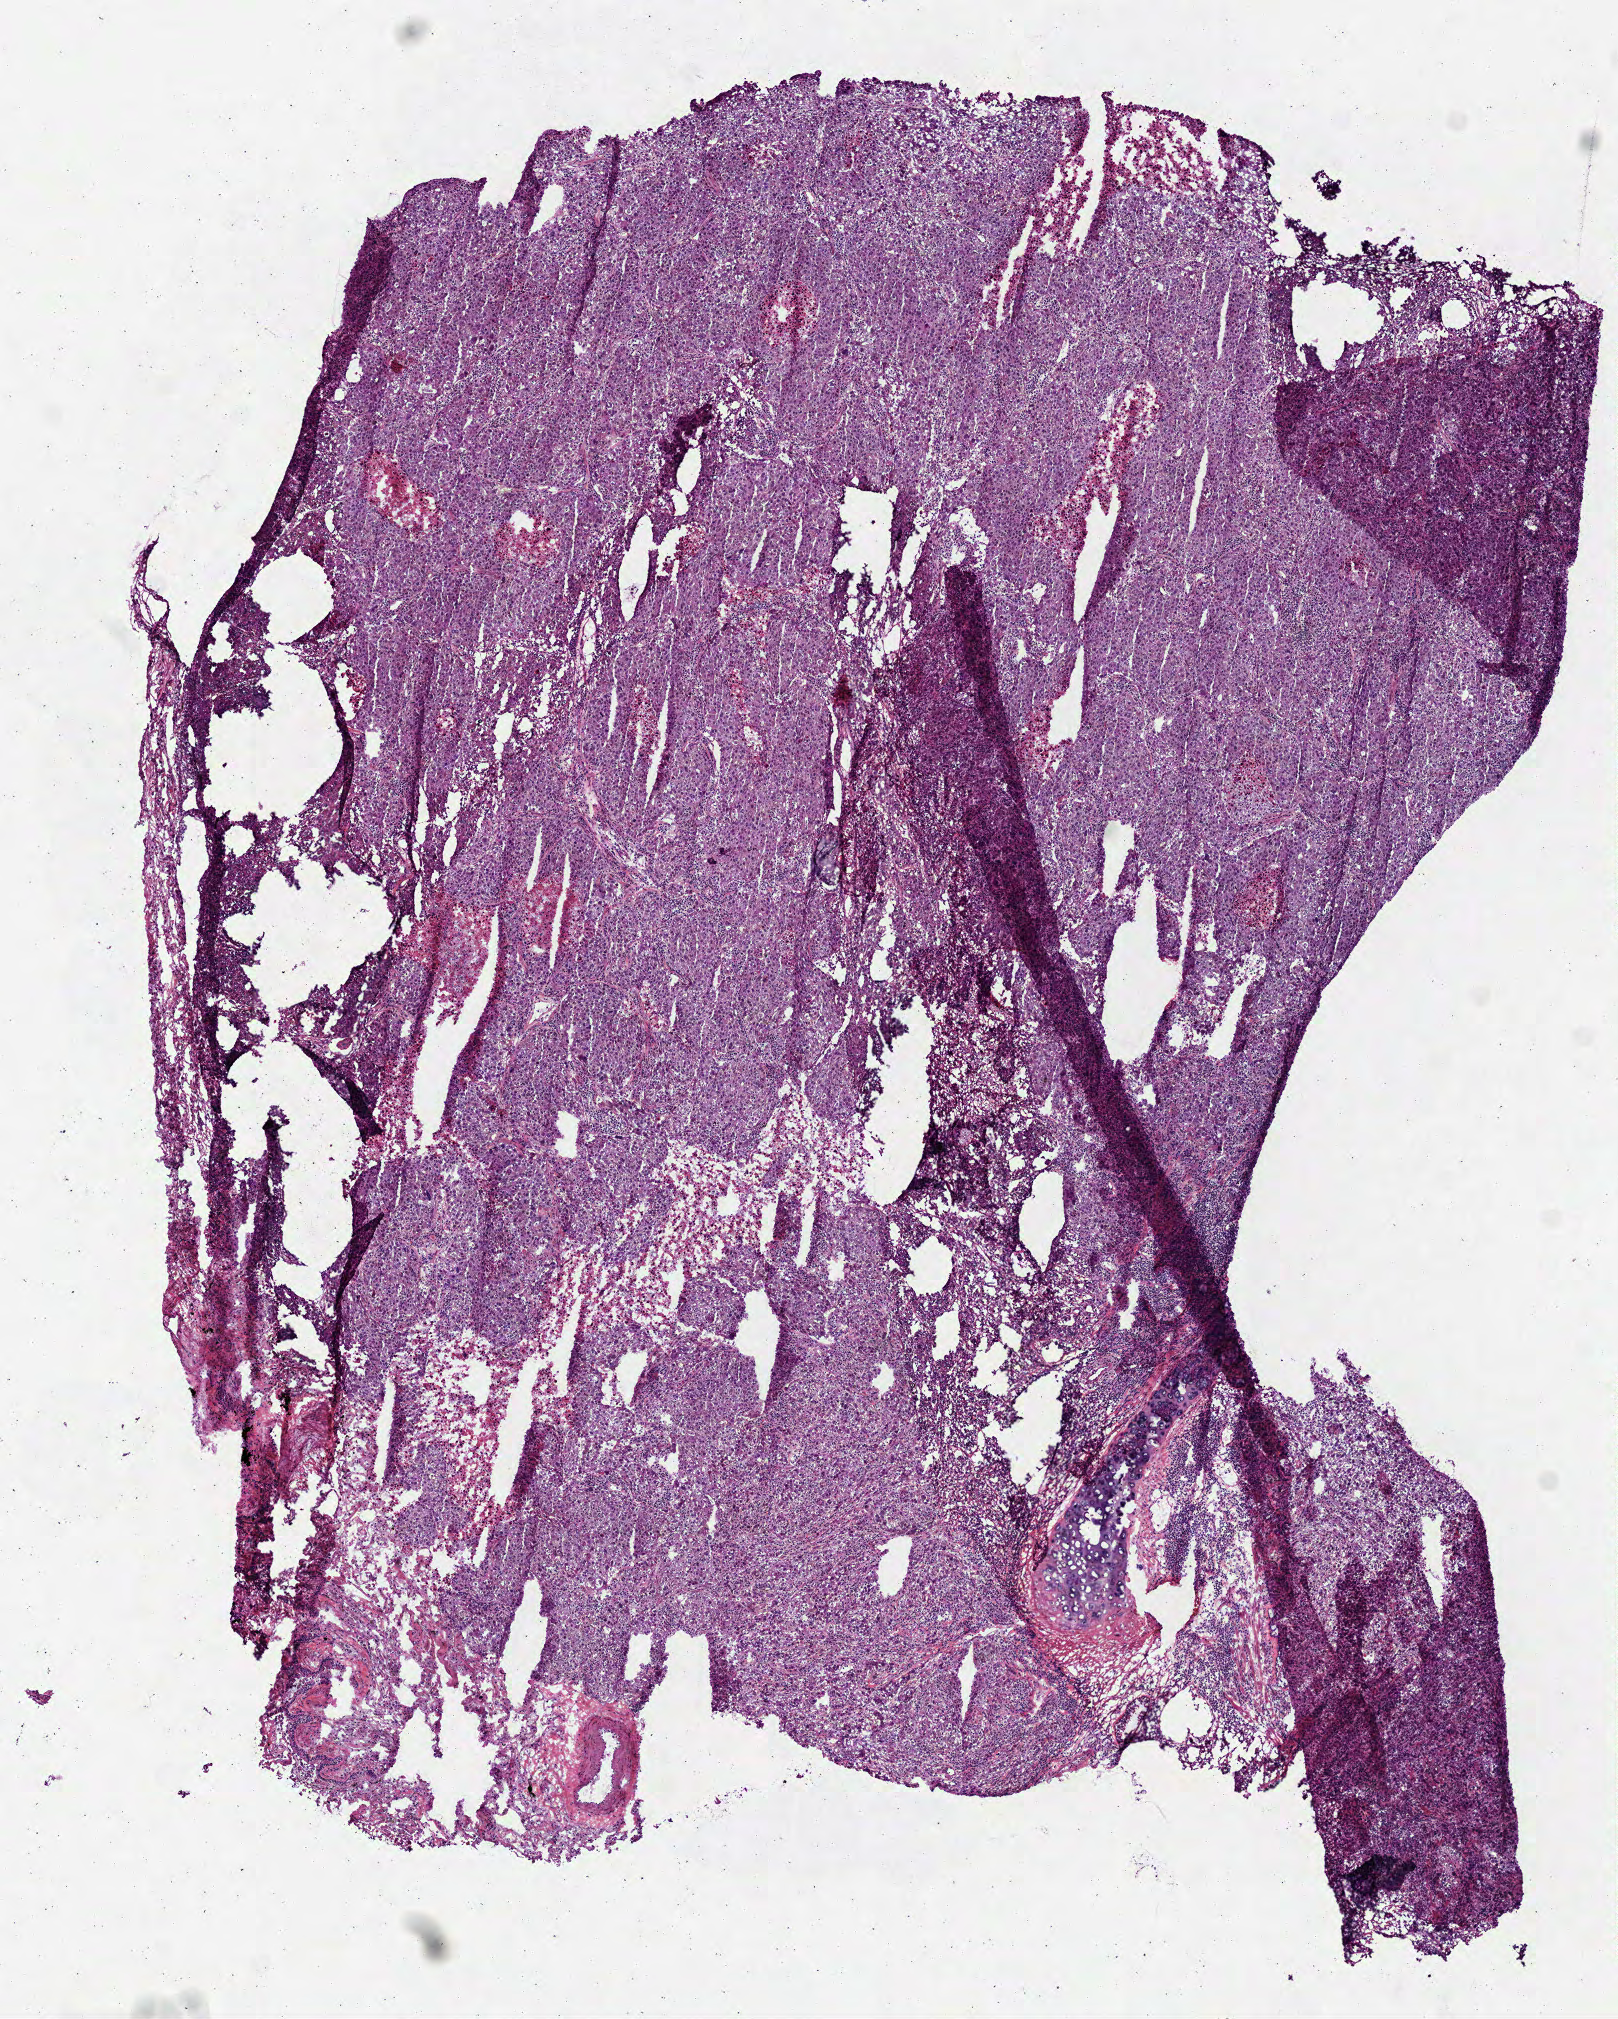
Whole-slide histology image, H&E-stained — a low-resolution overview of the entire scanned area, about 6.5 x 8.1 mm. Frozen section. Sample: primary tumour, lung. Patient: male, age at initial diagnosis 81 years. Composition of this section per pathologist review: tumour cells 5%, tumour nuclei 5%, normal cells 90%, stromal cells 5%, necrosis 0%.
AJCC pathologic stage: IIB (7th edition). Pathologic diagnosis: Adenocarcinoma, NOS. TNM: T3 N0 MX.